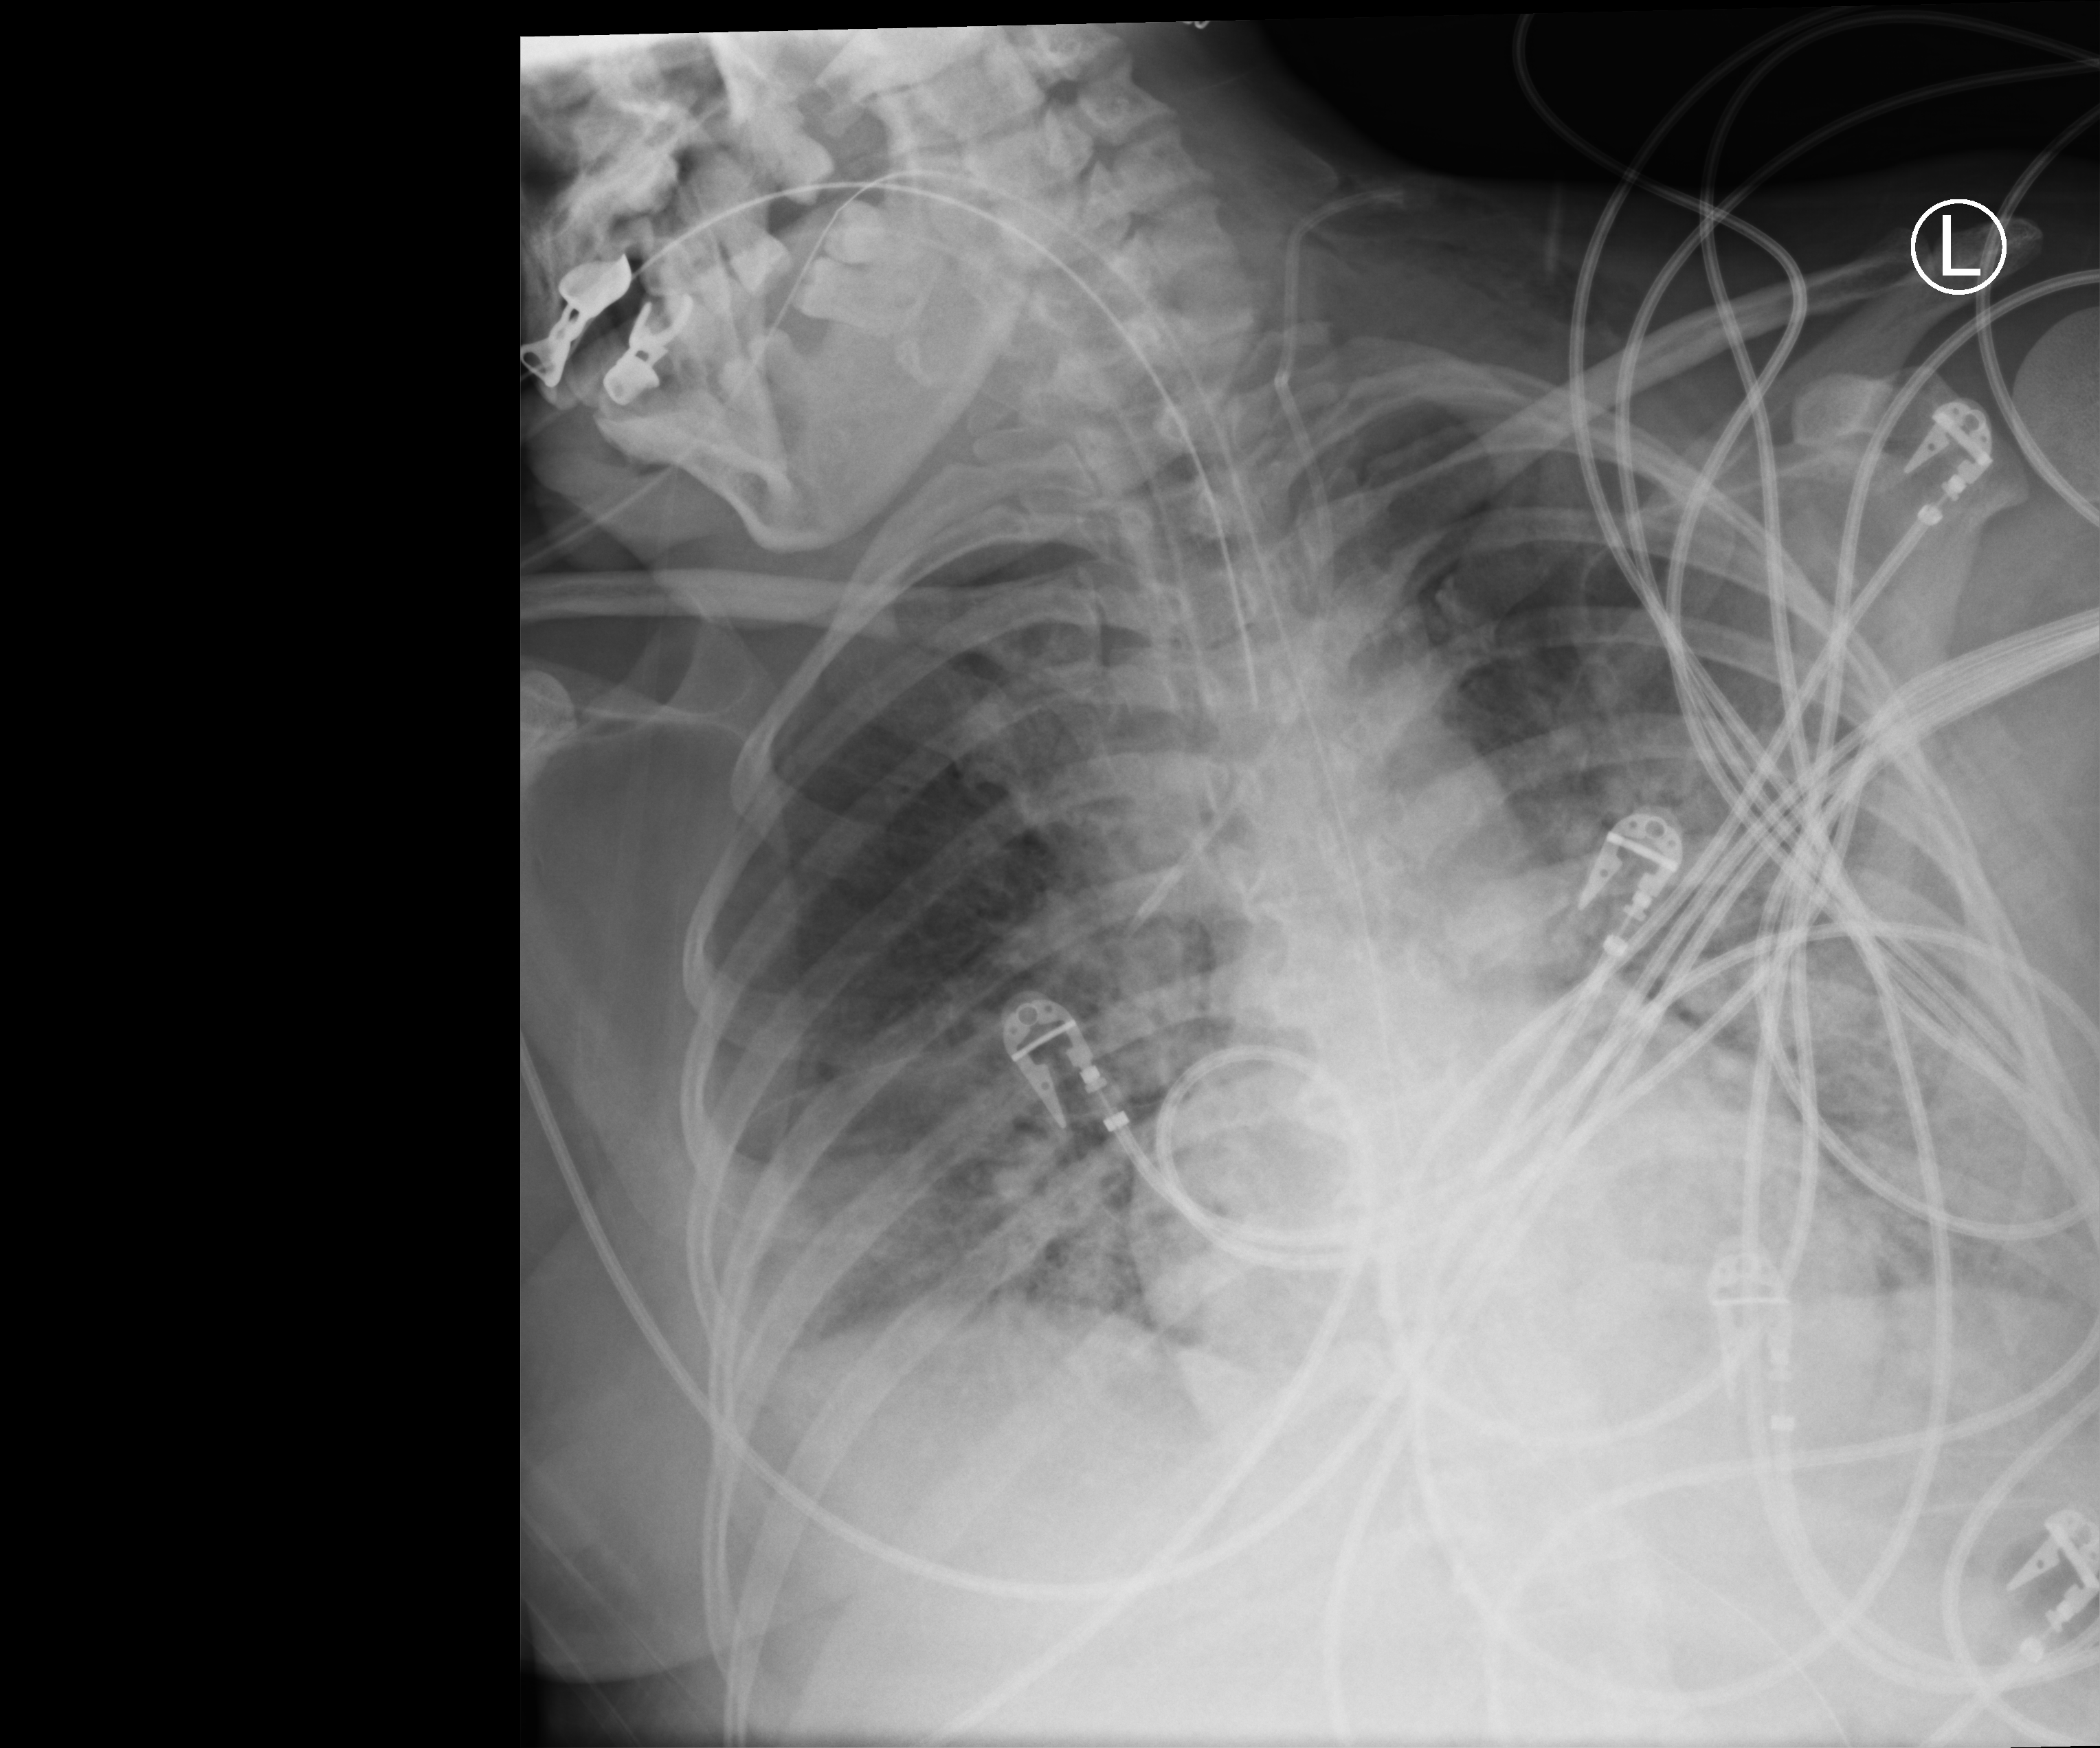
Portable chest radiograph; anteroposterior (AP) projection. Patient hospitalised with COVID-19; female, aged 18–59 years.
Admission-level facts for this patient (not findings on this image; timing relative to this image not recorded): length of hospital stay: 71 days; hypertension (admission record): no.